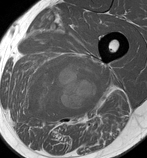
MRI of an extremity soft-tissue mass, one axial slice. Slice 74 of 86 in the series (ordered by position). MR volume resampled by the dataset authors to the PET/CT grid (not the native acquisition matrix). 3.27 mm slice thickness. 147 × 158 image matrix, field of view 144 × 154 mm. Male patient. From the clinical record (not read from this slice): histological type: undifferentiated pleomorphic liposarcoma; grade: high; site of the primary tumour: left thigh.
Structures marked on this image (expert contour drawn on MRI and transferred to this co-registered scan by the dataset authors):
- gross tumour volume including surrounding oedema: box from (x=21, y=60) to (x=109, y=125) px
- gross tumour volume (mass): (x=30, y=63)–(x=104, y=120)